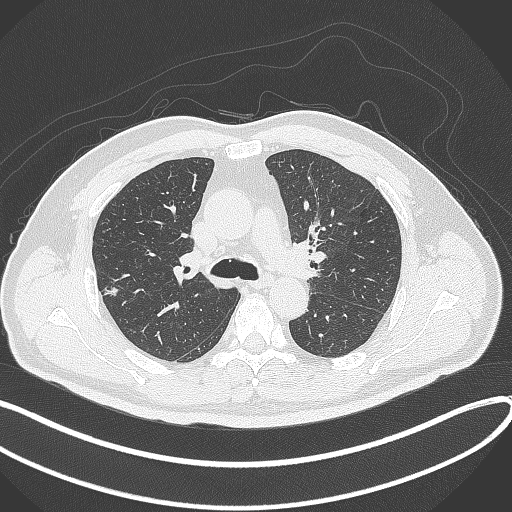
Chest CT, one axial slice. Position 224 of 372 along the scan axis. Reconstruction kernel B70f. 120 kVp. Lung window (W 1500 / L -600 HU). 1 mm slice thickness. 512 × 512 image matrix, field of view 400 × 400 mm. Male patient, age 60 years. Case-level facts recorded for this patient, not image findings: clinical TNM (as recorded): T1c N0 M0.
Outlined on this slice (rectangle marked by the reading radiologist):
- lung tumour (recorded histology: adenocarcinoma): bounding box [x1, y1, x2, y2] px = [99, 283, 123, 301]